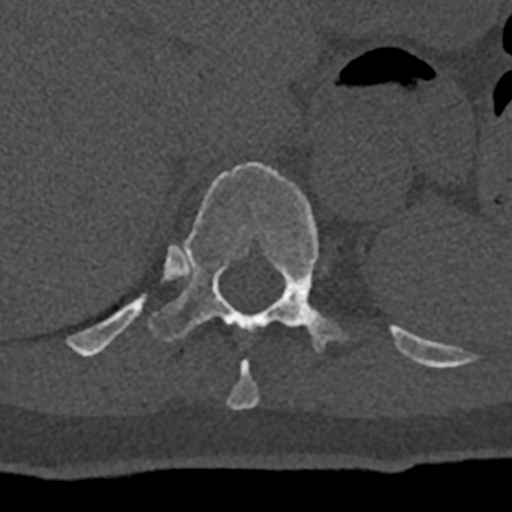
CT including the spine, one axial slice. Slice 553 of 797 in the series (ordered by position). 120 kVp. Bone window (W 1800 / L 400 HU). 0.5 mm slice thickness. 512 × 512 image matrix. Male patient, age 74 years. Case-level facts recorded for this patient, not image findings: primary cancer: renal; vertebrae with lytic lesions (as recorded): T10, L1, L2, L3, L4, L5.
Outlined on this slice (semi-automatic segmentation, software-assisted and operator-edited):
- T10 vertebra: bounding box [x1, y1, x2, y2] px = [226, 359, 260, 409]
- T11 vertebra: [70, 162, 432, 367]